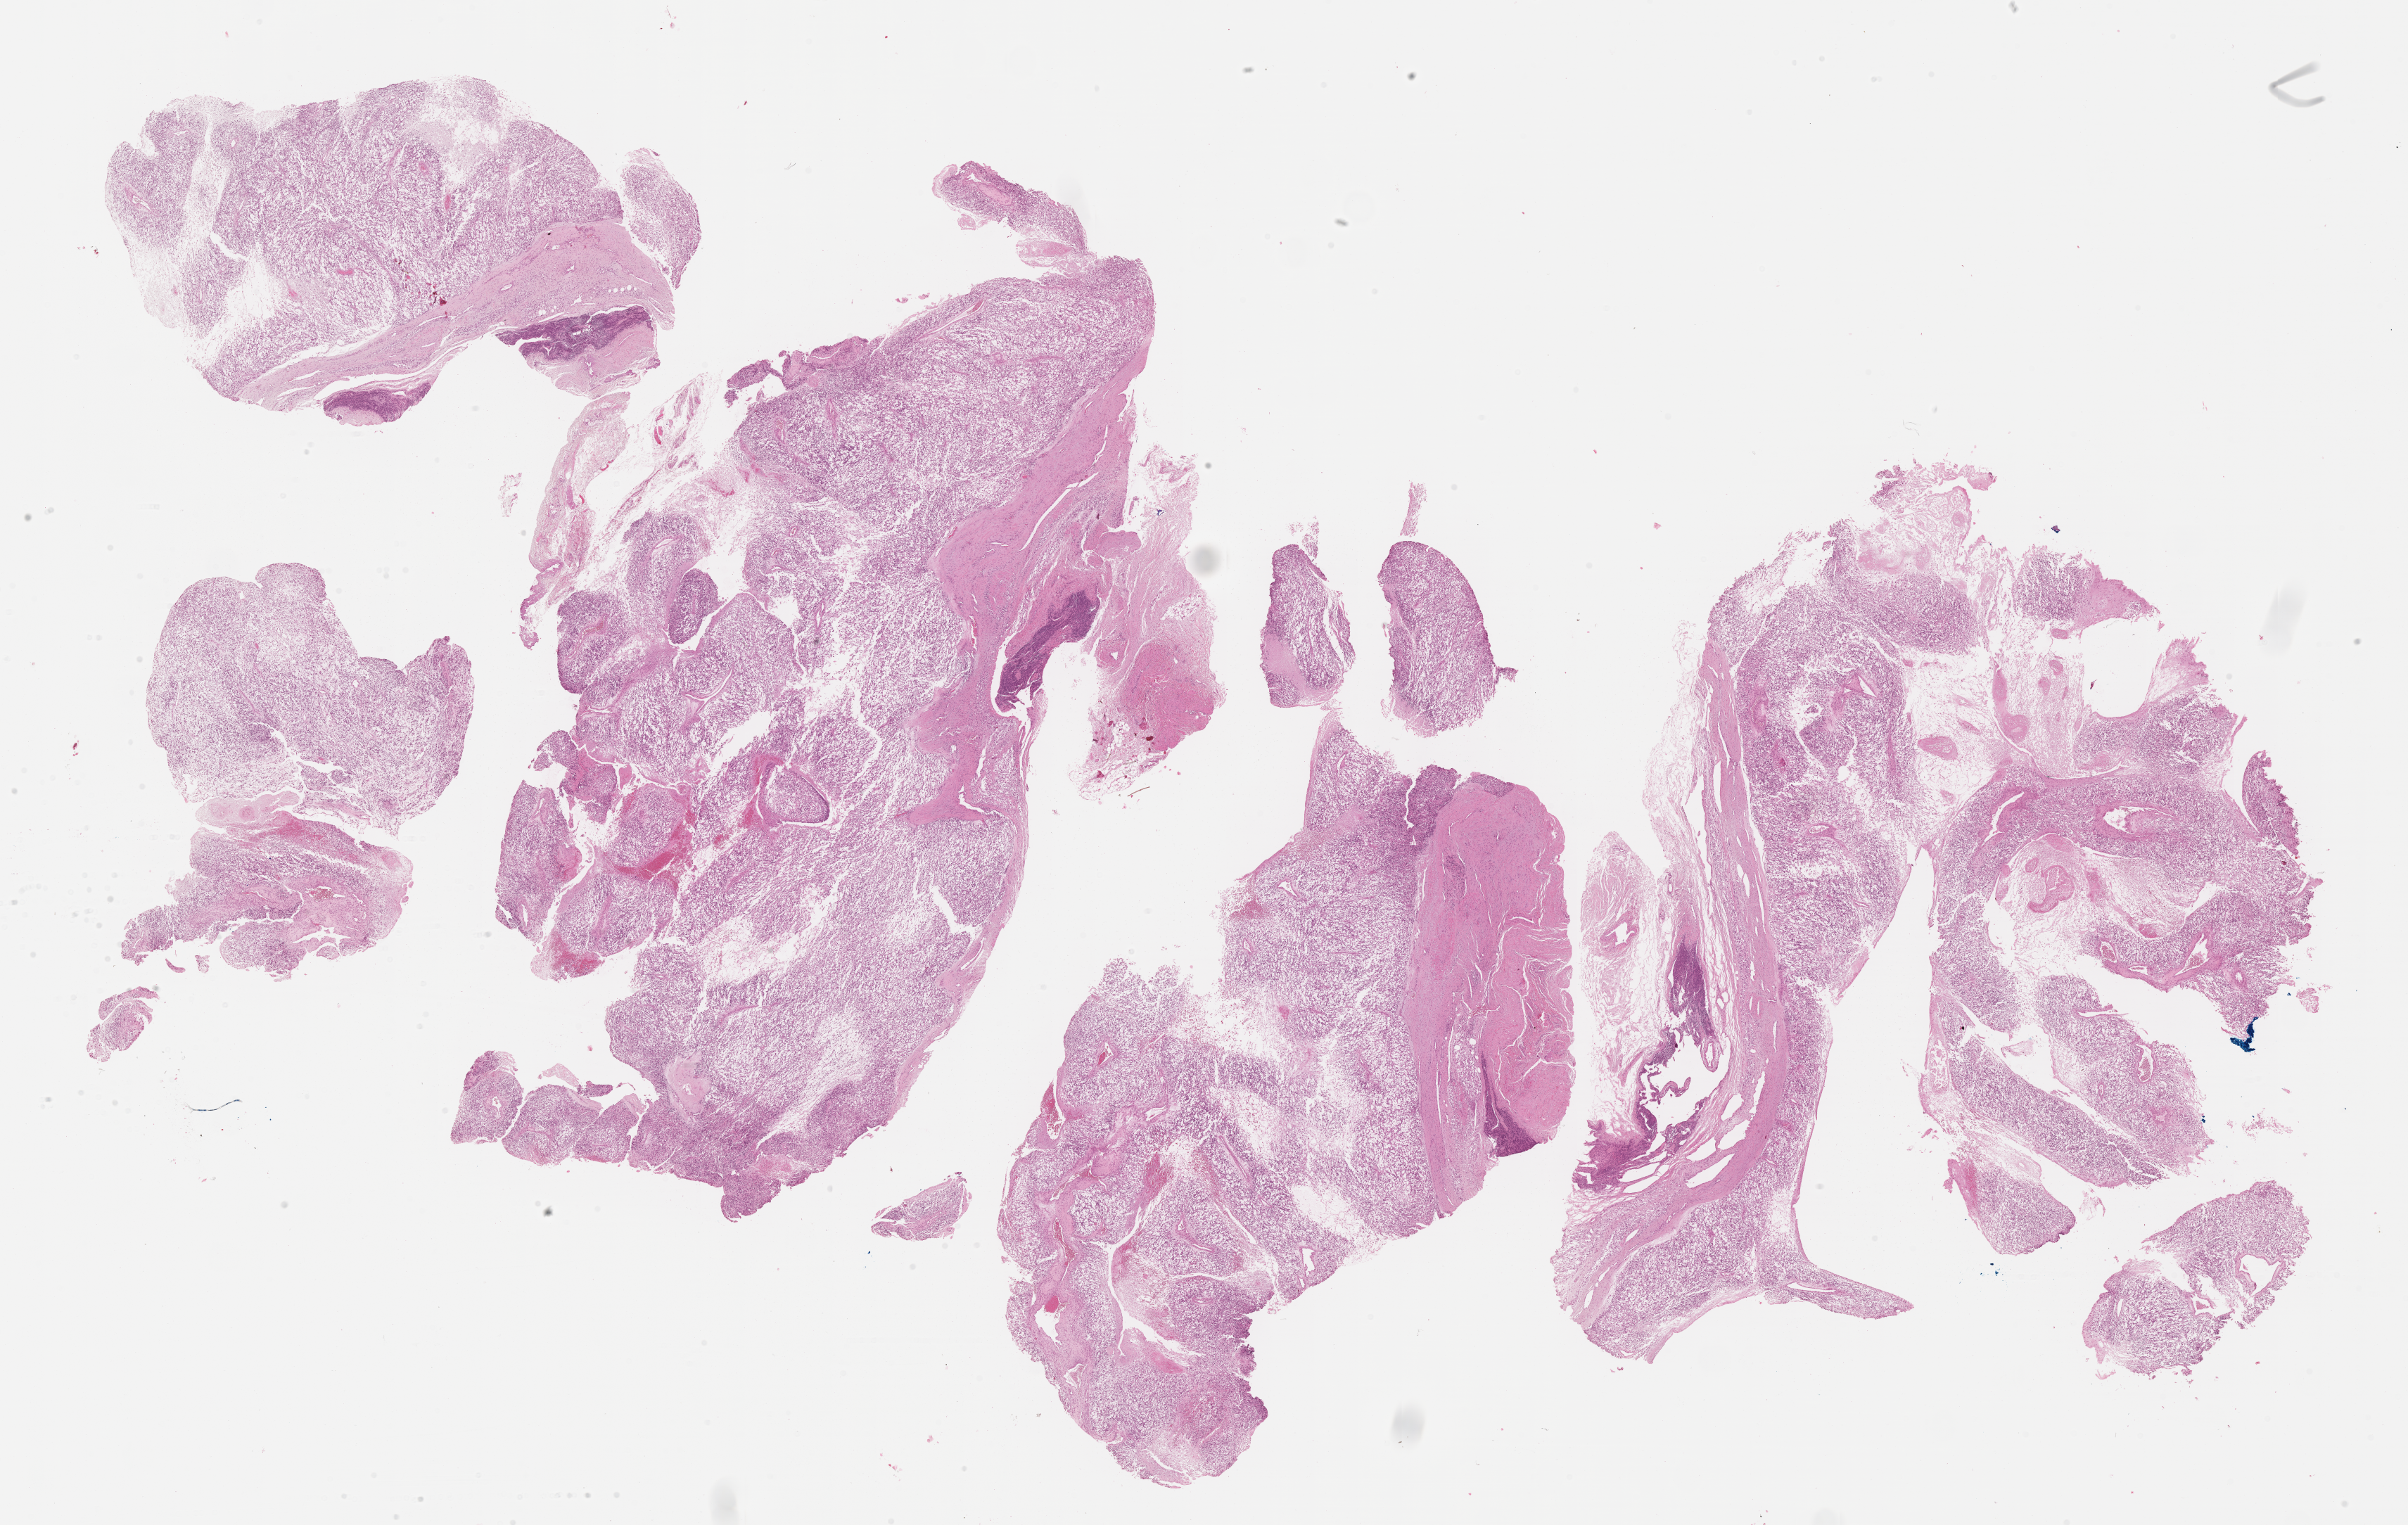
H&E whole-slide image of tumor tissue — low-resolution overview of the scanned area, about 27.7 x 17.5 mm; formalin-fixed paraffin-embedded section; sample anatomic site: pelvis. Patient: male, age 6.4 years at diagnosis.
* metastatic status at presentation (as recorded): non-metastatic
* stage (as recorded): 3
* diagnosis: rhabdomyosarcoma; histological classification: embryonal rhabdomyosarcoma